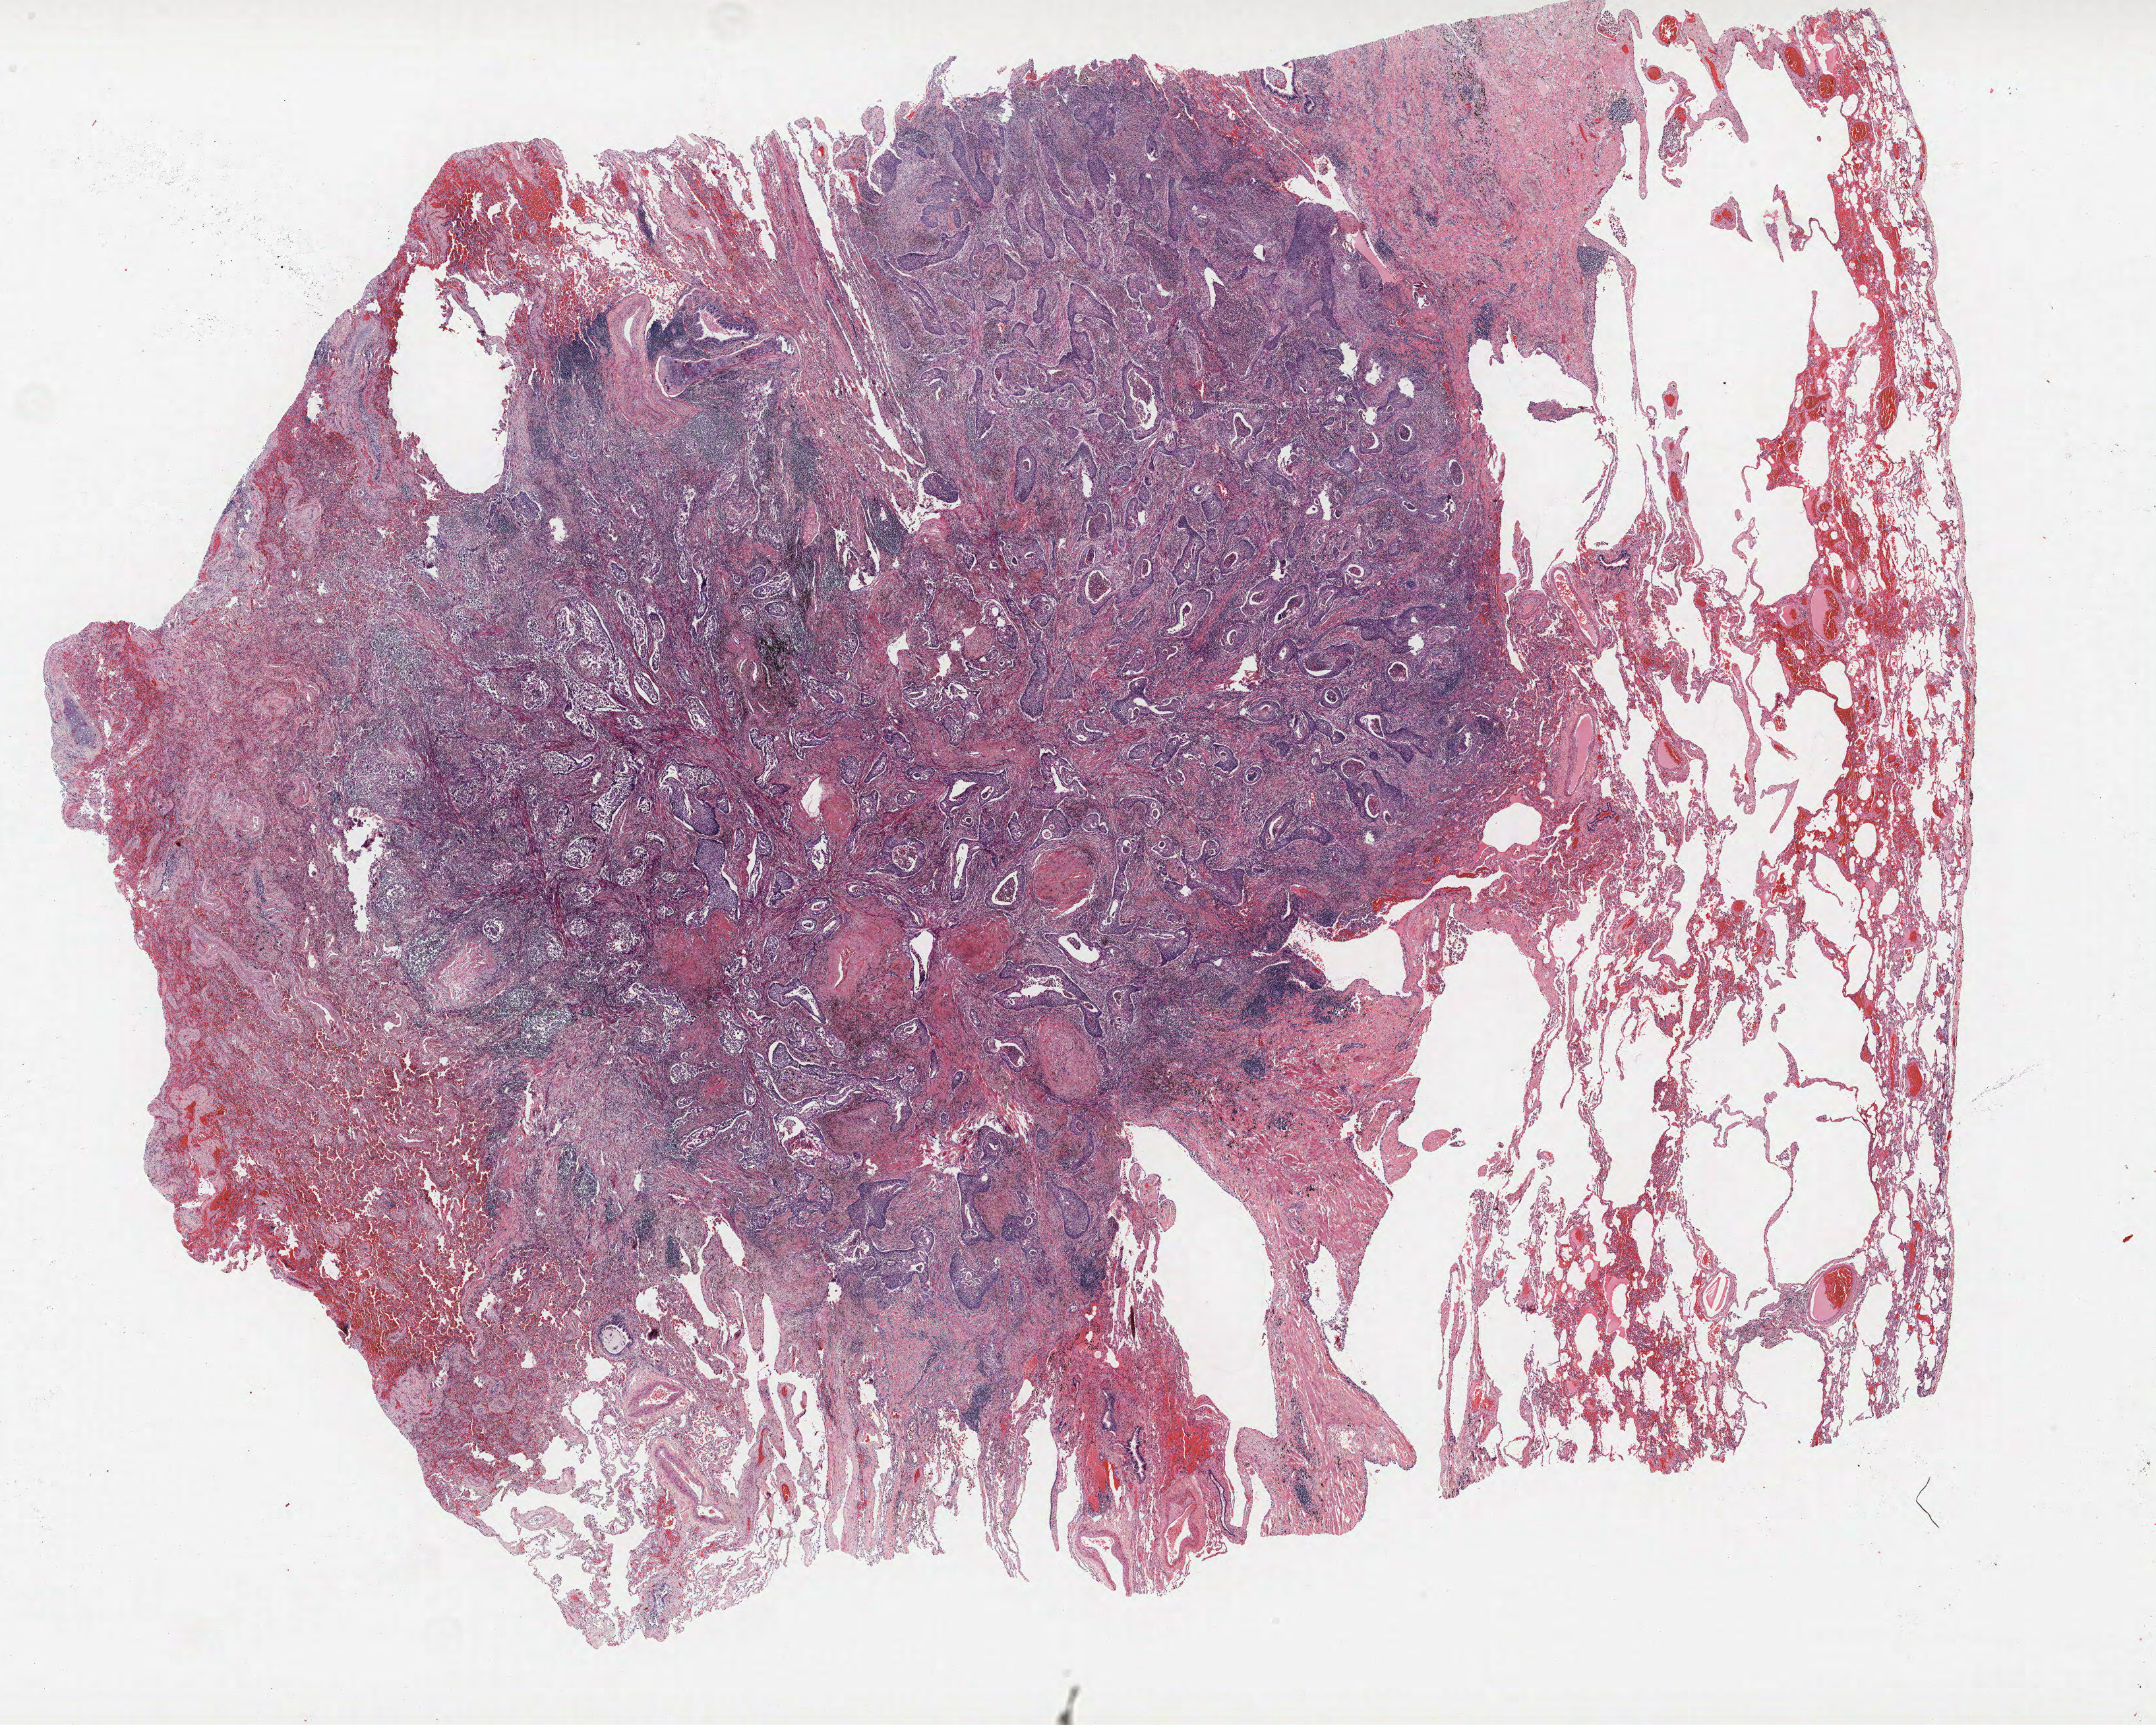
Hematoxylin and eosin (H&E) stained whole-slide image — shown as a low-resolution overview of the whole scanned area (about 26.2 x 20.9 mm, slide scanned at 40x). Formalin-fixed paraffin-embedded (FFPE) section. Lung tissue. Female, age 64 at enrolment. Grade: moderately differentiated (G2).
• ICD-O-3 topography: upper lobe of lung (C34.1)
• participant's lung-cancer diagnosis: Squamous cell carcinoma, NOS
• stage (AJCC 6th edition): IA
• tumour size (pathology): 15 mm
• primary tumour location (clinical record): left upper lobe